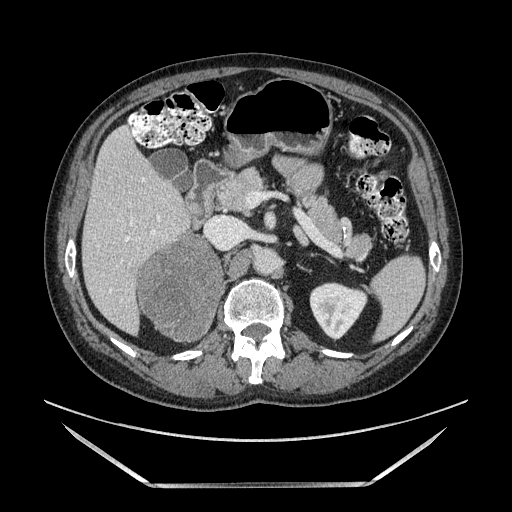
Contrast-enhanced abdominal CT, one axial slice. Position 75 of 185 along the scan axis. Soft-tissue window (W 400 / L 40 HU). 1.25 mm slice thickness. 512 × 512 image matrix, field of view 440 × 440 mm. Male patient. Case-level facts recorded for this patient, not image findings: diagnosis: adrenocortical carcinoma; tumour side: right adrenal; tumour size at pathology: 10.3 cm; Ki-67 index: 20 %.
Outlined on this slice (semi-automatic segmentation, software-assisted and operator-edited):
- mass: box from (x=141, y=235) to (x=223, y=339) px